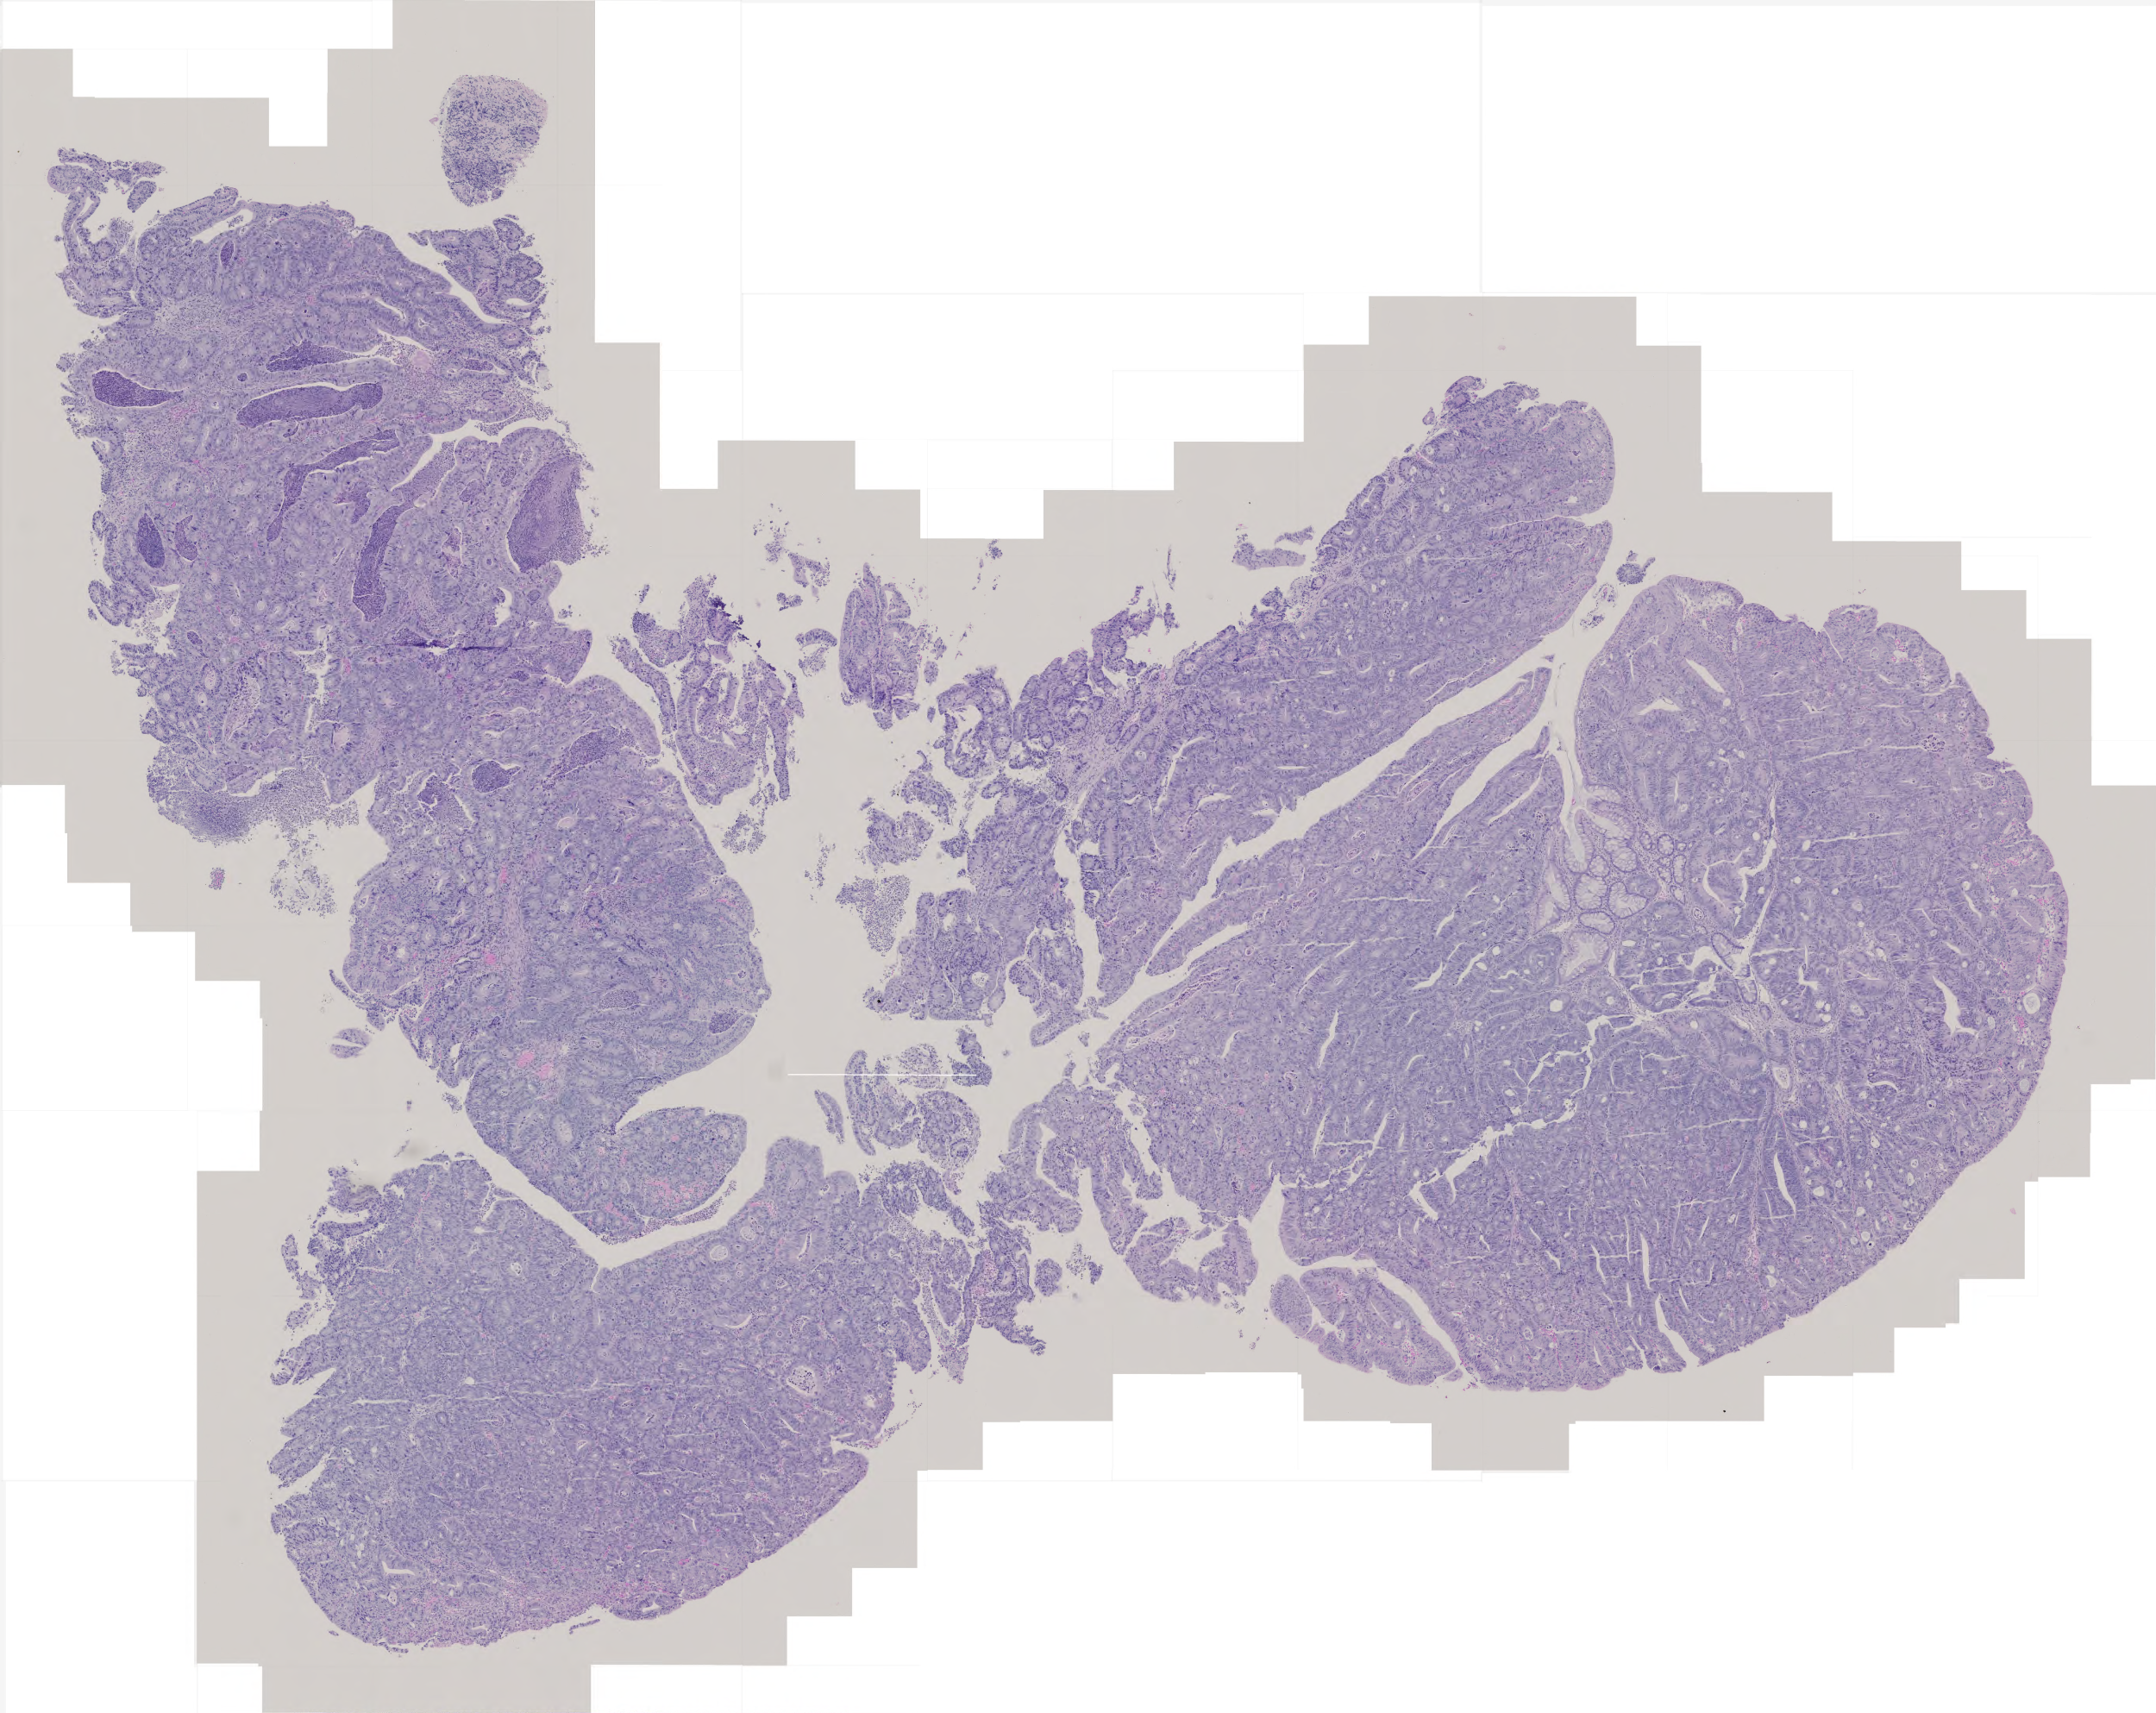
Hematoxylin and eosin (H&E) stained whole-slide image — a low-resolution overview of the entire scanned area, about 5.0 x 4.0 mm. Formalin-fixed paraffin-embedded (FFPE) diagnostic section. Sample: primary tumour, colon. Patient: female, age at initial diagnosis 80 years.
- AJCC pathologic stage: IV (5th edition)
- histologic diagnosis: Adenocarcinoma, NOS
- TNM: T4 N2 M1